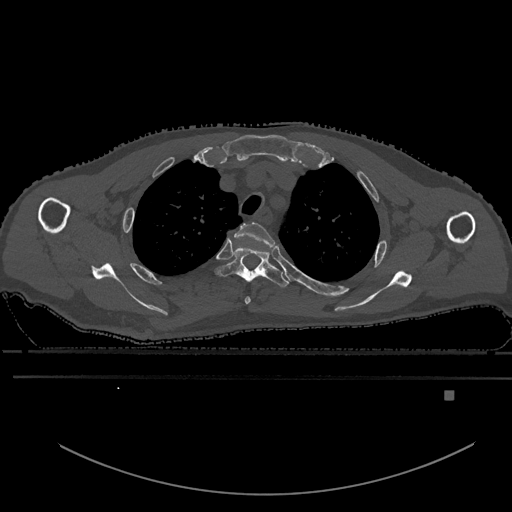
CT including the spine, one axial slice; position 464 of 969 along the scan axis; bone window (W 1800 / L 400 HU); 0.5 mm slice thickness; 512 × 512 image matrix, field of view 456 × 456 mm. Patient: male, 82 years. Case-level facts recorded for this patient, not image findings: primary cancer: prostate.
Annotated regions visible in this slice (semi-automatically segmented with operator editing):
- T2 vertebra: box from (x=235, y=221) to (x=275, y=305) px
- T3 vertebra: (x=215, y=248)–(x=289, y=287)